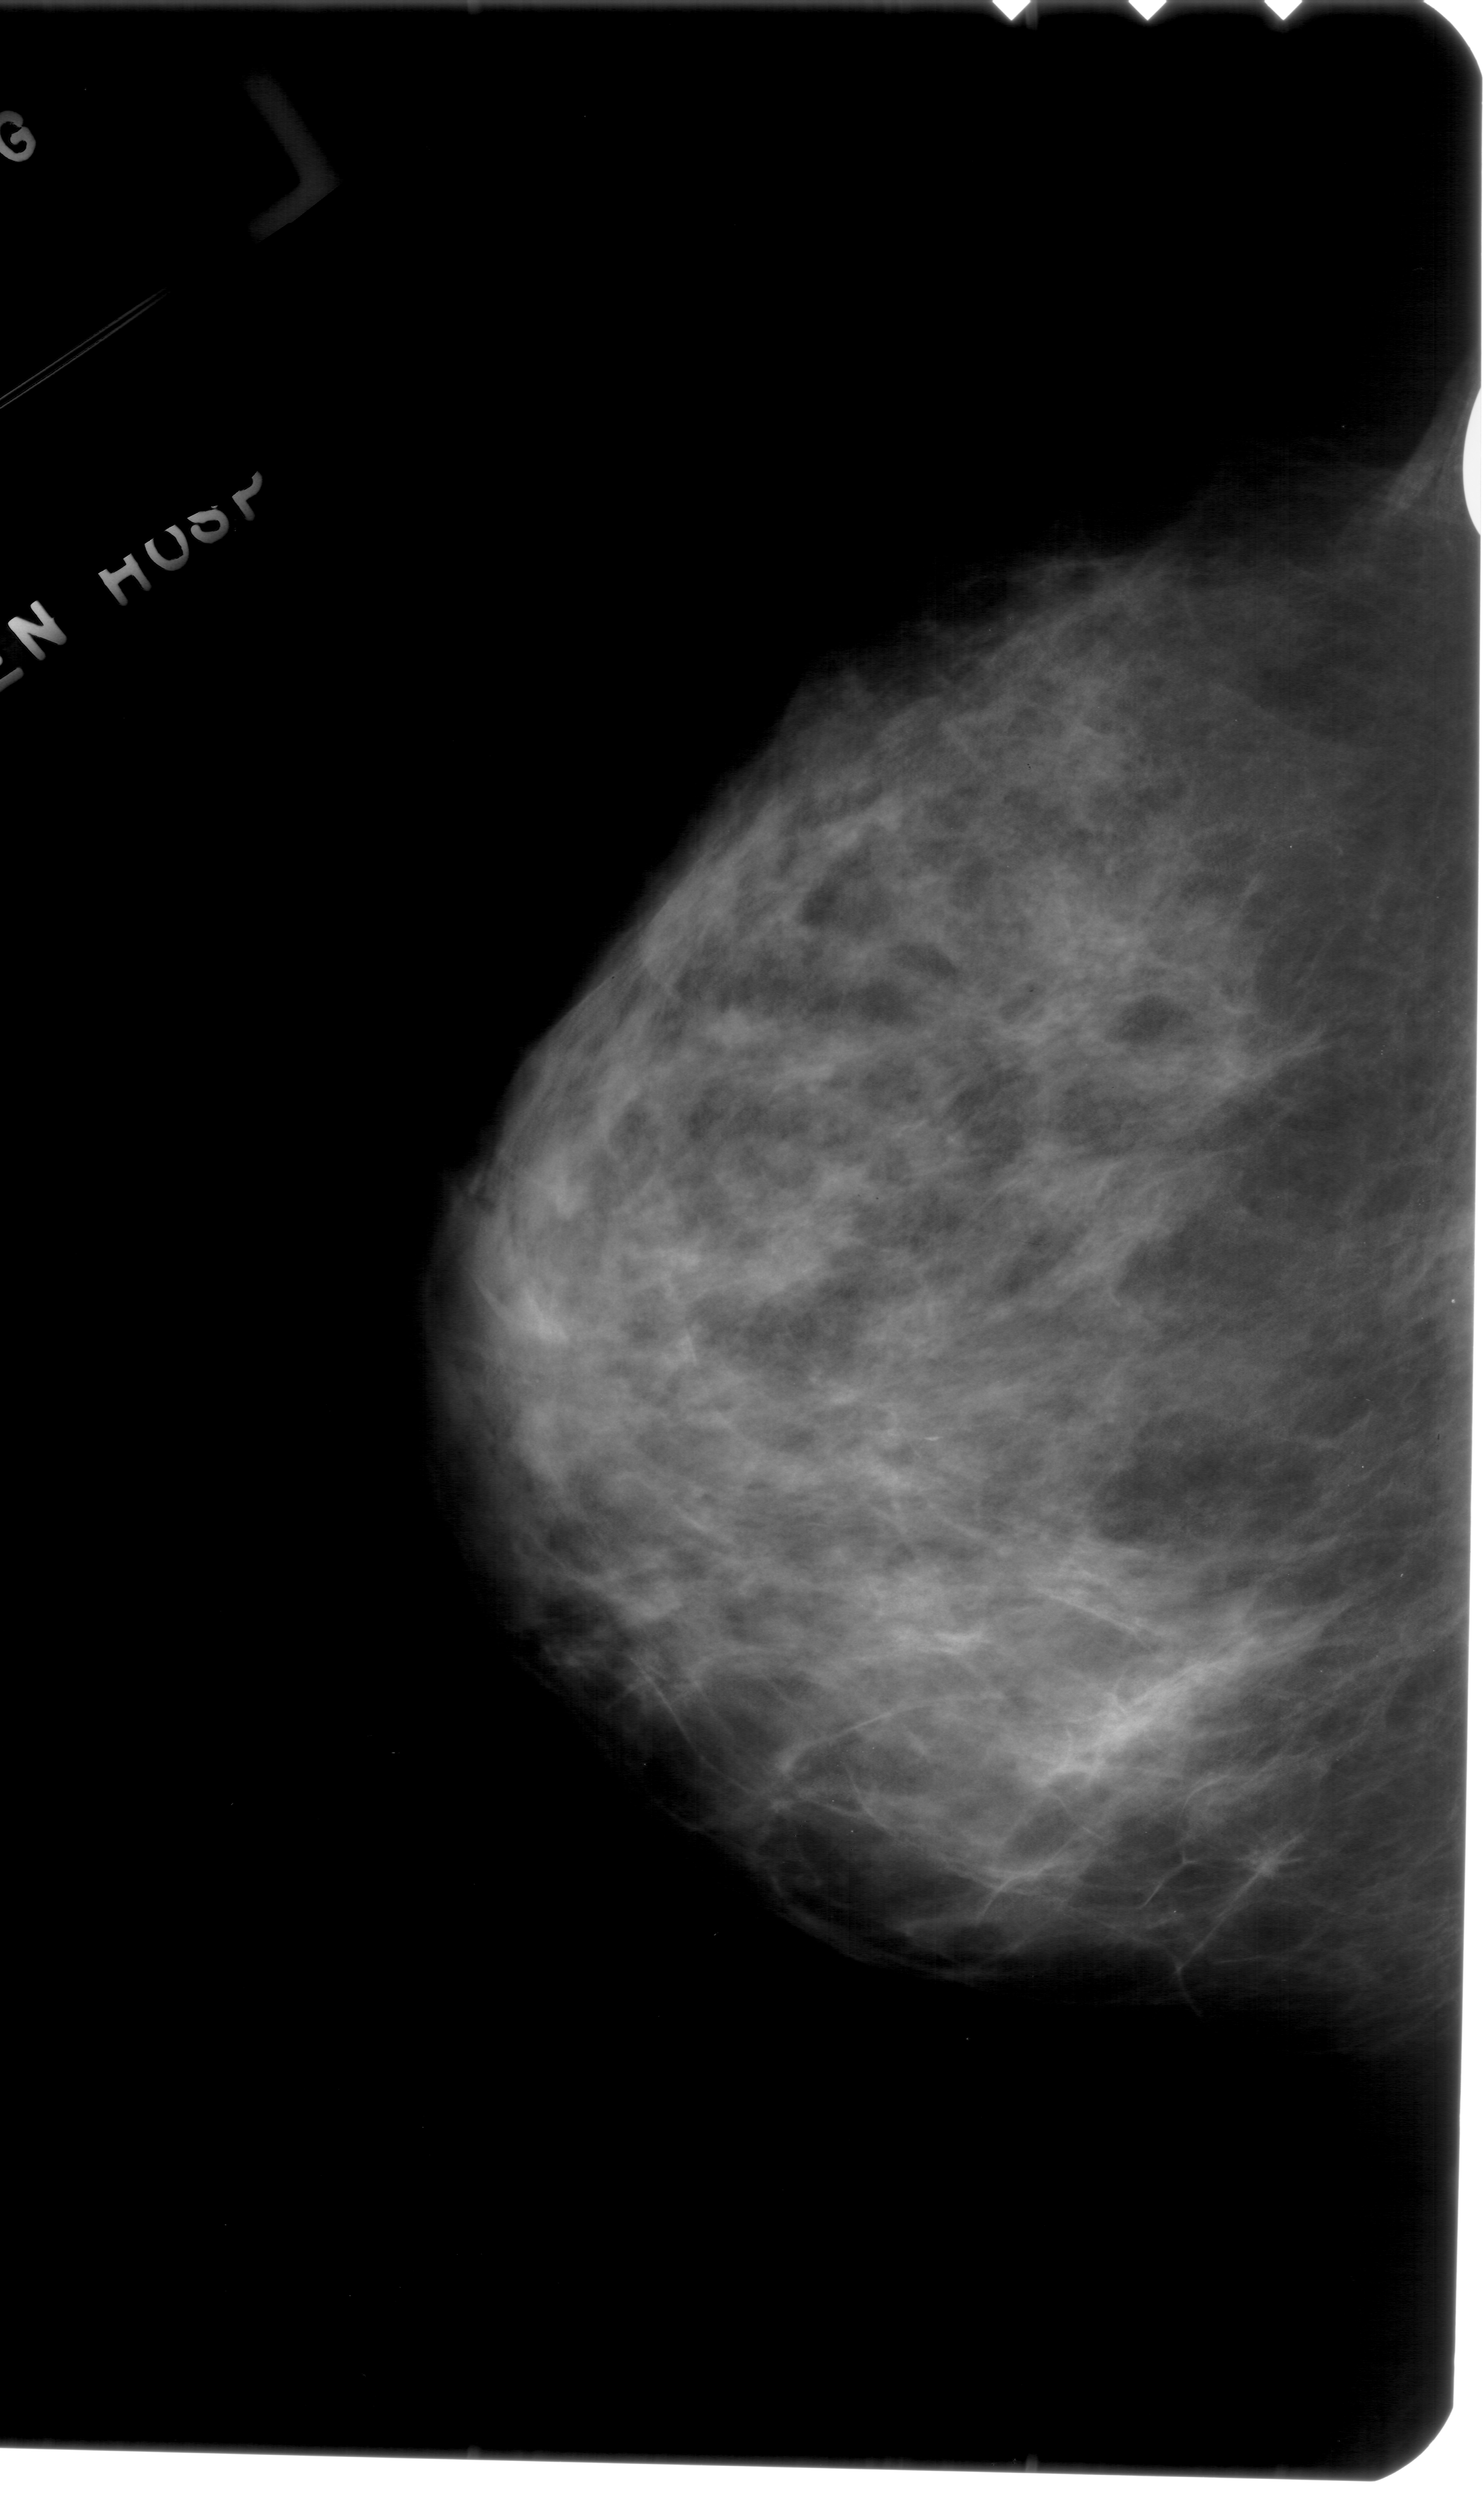
Digitized screen-film mammogram; left breast; craniocaudal (CC) view; BI-RADS breast density category 3 (scale 1–4); 1484 × 2503 image matrix.
Expert-marked regions of interest on this image (one box per marked abnormality):
- calcifications, morphology fine linear branching, distribution linear; BI-RADS assessment category 4; pathology result (as recorded, not read from the image): malignant: bounding box (x1, y1, x2, y2) in pixels: (859, 1409, 944, 1465)